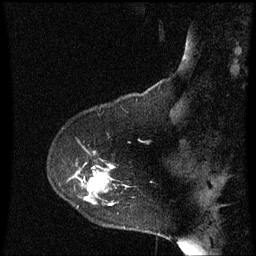
Breast MRI (dynamic contrast-enhanced), one sagittal slice; slice 15 of 60 in the series (ordered by position); dynamic contrast-enhanced series, image 2 of 3 at this slice position (ordered by acquisition); 1.5 T; TE 4.2 ms, TR 8.9 ms; 2 mm slice thickness; 256 × 256 image matrix. Female patient, age 53 years. Case-level facts recorded for this patient, not image findings: setting: breast cancer imaged before/during neoadjuvant chemotherapy; receptor status: HR-positive, HER2-negative.
Annotated regions visible in this slice (semi-automatic segmentation, software-assisted and operator-edited):
- analysis volume of interest (the breast-tissue region the enhancement analysis was run in; not a lesion): box from (x=78, y=164) to (x=131, y=231) px
- tumour enhancement mask (voxels above the 70 % enhancement threshold inside the analysis volume of interest): (x=86, y=166)–(x=113, y=201)